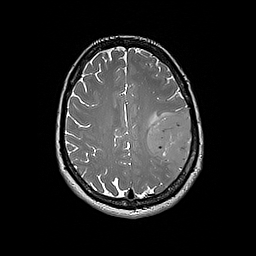
Brain MRI from a brain-tumour surgery series, one axial slice; position 71 of 192 along the scan axis; 1 mm slice thickness; 256 × 256 image matrix, field of view 250 × 250 mm. From the clinical record (not read from this slice): histopathology: Glioblastoma; WHO grade: 4; IDH mutation: no; tumour location: Left Frontal.
Annotated regions visible in this slice (manually delineated by an expert):
- tumour: bounding box (x1, y1, x2, y2) in pixels: (147, 114, 193, 165)